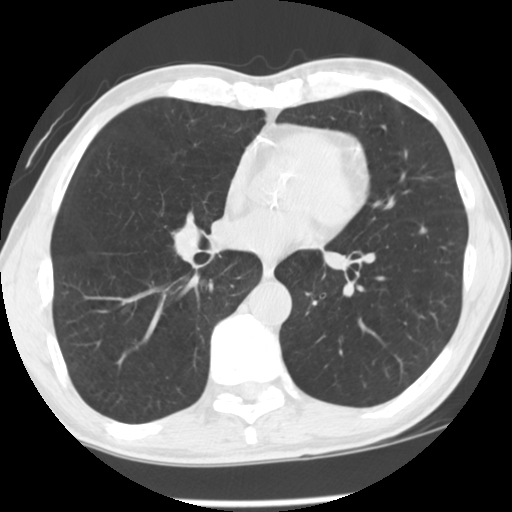
Low-dose screening chest CT, one axial slice. Slice 63 of 139 in the series (ordered by position). Reconstruction kernel STANDARD. 120 kVp. Lung window (W 1500 / L -600 HU). 2.5 mm slice thickness. 512 × 512 image matrix, field of view 320 × 320 mm.
Structures marked on this image (manually delineated by an expert):
- lesion 1 (tumor, lower lobe of left lung): bounding box [x1, y1, x2, y2] px = [422, 228, 424, 232]